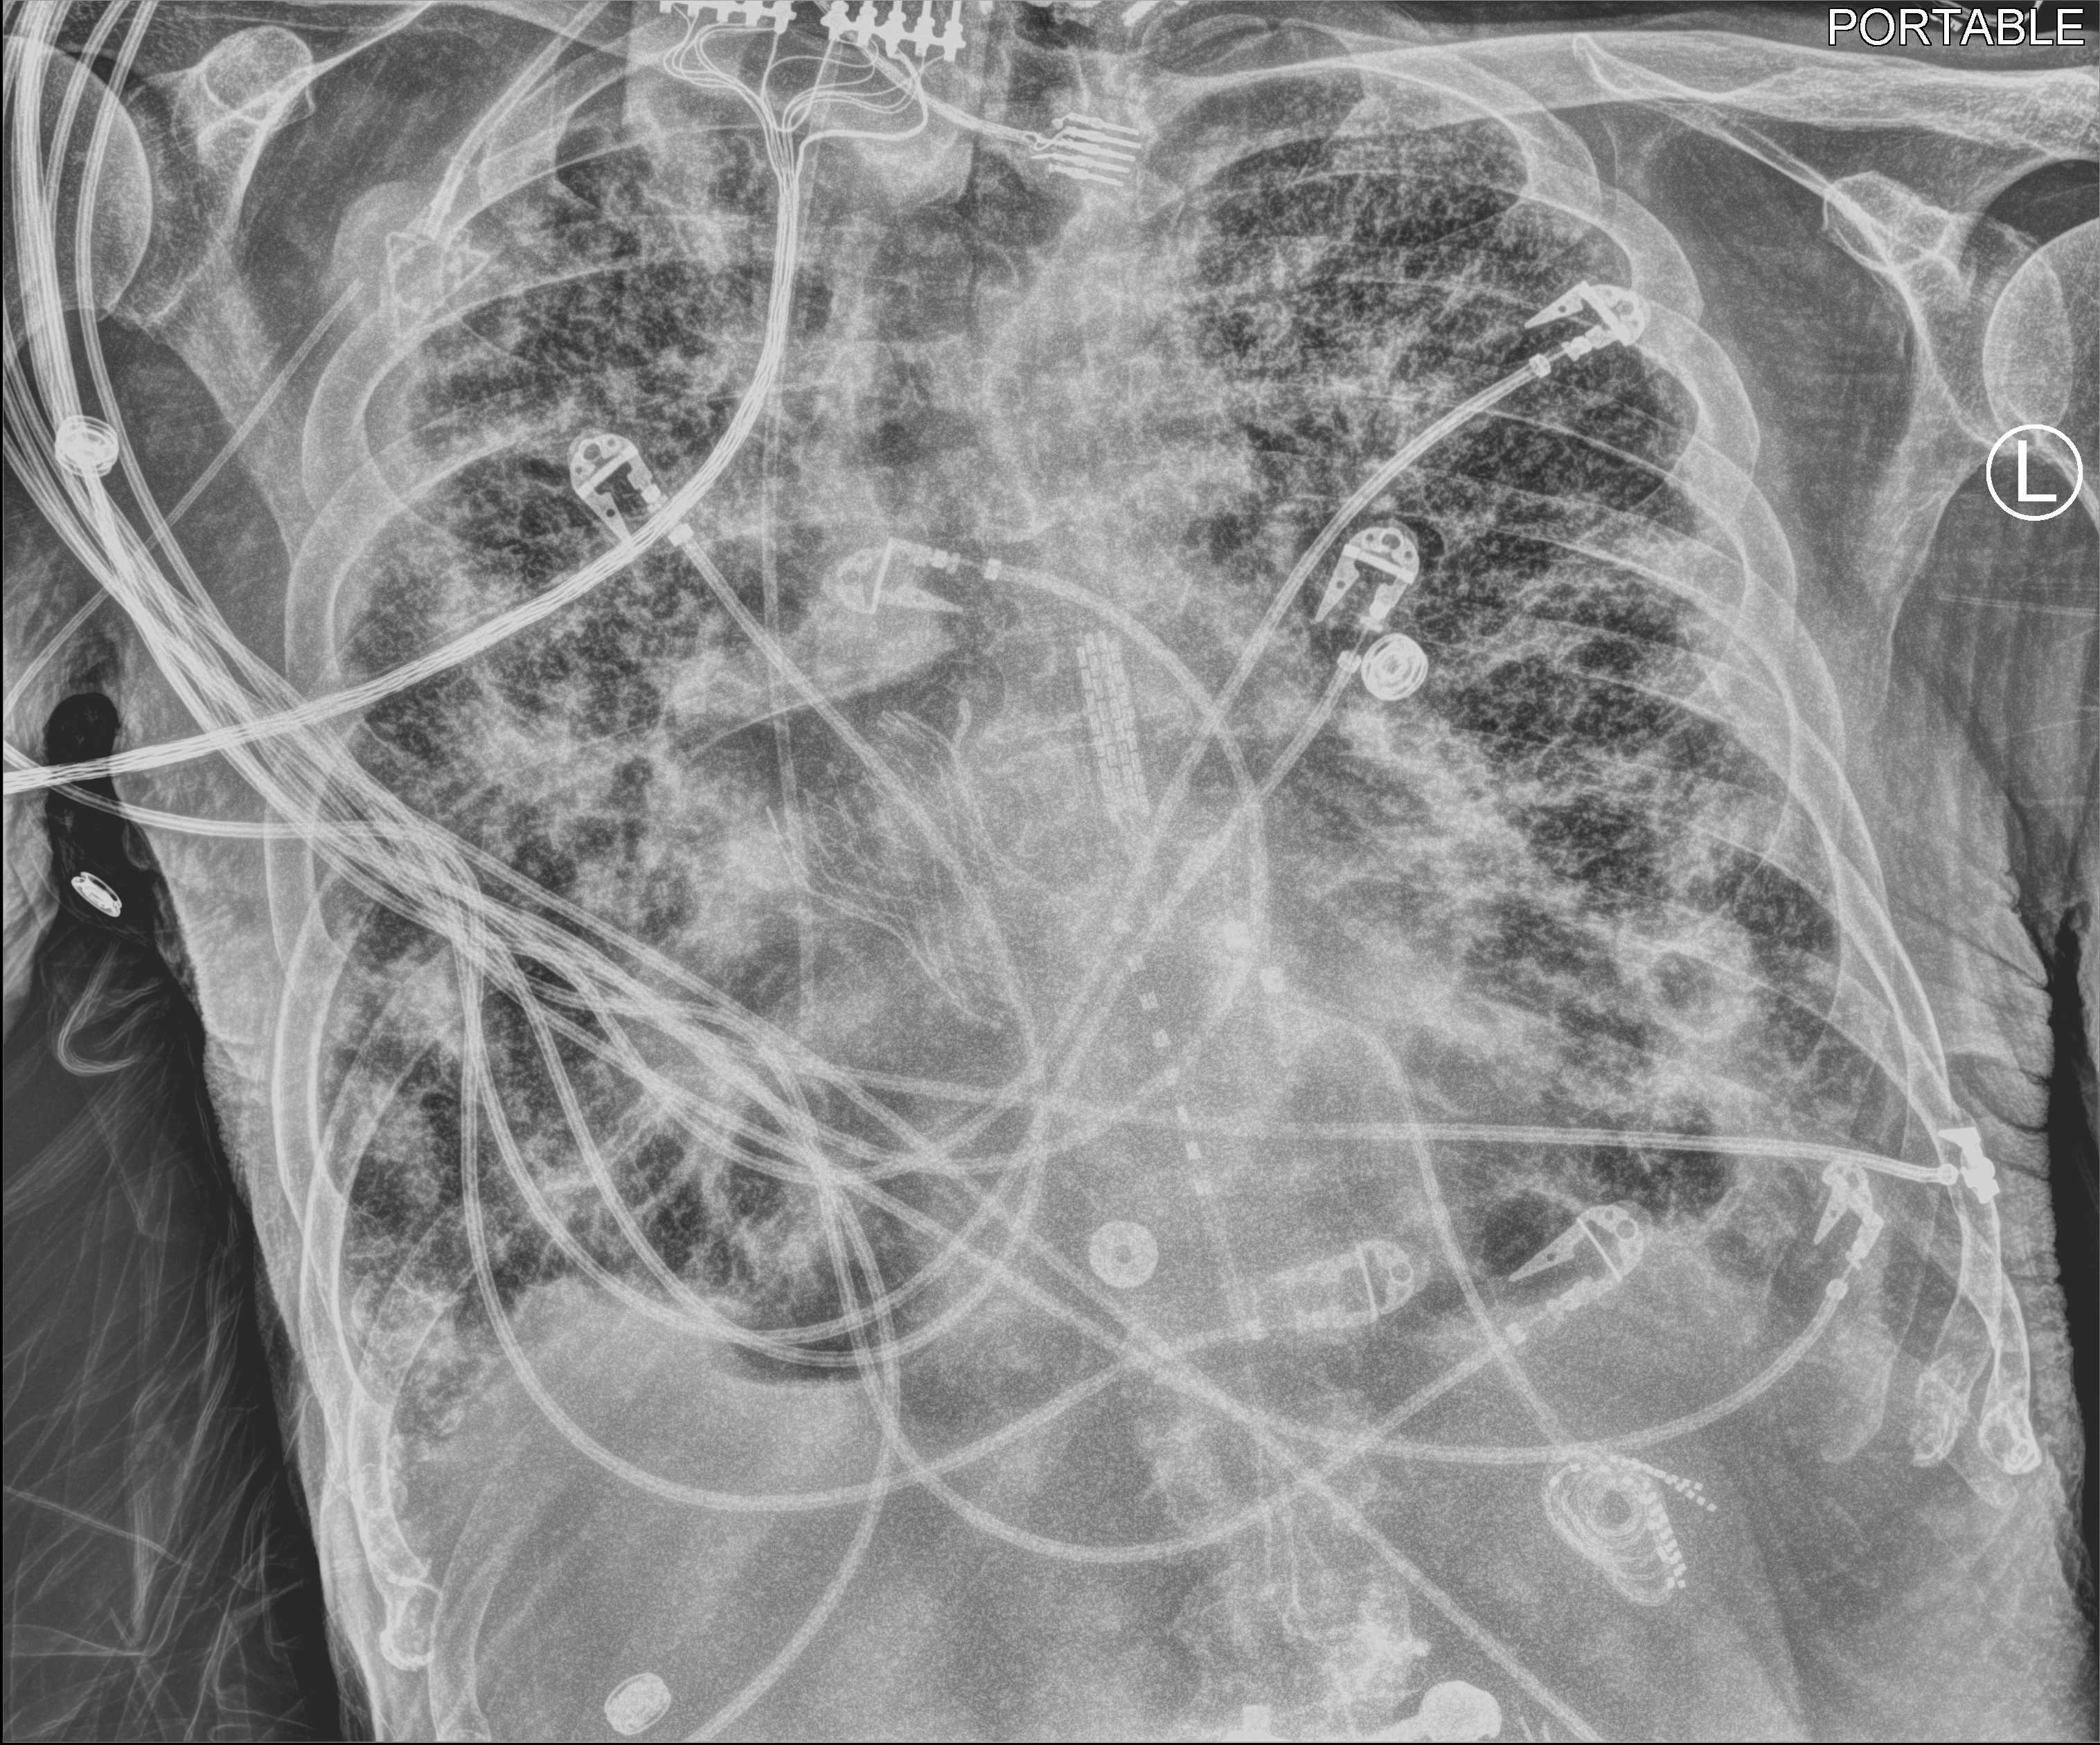
Portable chest radiograph, anteroposterior (AP) projection. Patient hospitalised with COVID-19; male, aged 75–90 years.
From the hospital-stay record, not from the radiograph (when in the stay this image was taken is not recorded):
- mechanically ventilated during this hospital stay: no
- chronic kidney disease (admission record): yes